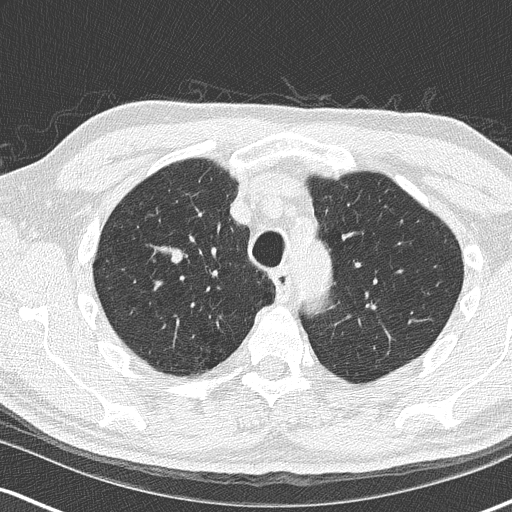
Axial slice from a low-dose chest CT screening exam, second screening round (one year after baseline), lung window (W 1500 / L -600 HU), 2 mm slice thickness, 120 kVp. Male, age 68 years at enrolment.
Expert-annotated lung lesion, bounding box [x1, y1, x2, y2] px = [152, 232, 215, 293]. Screening reader's record for this exam (one nodule recorded; not confirmed to be the boxed lesion): non-calcified nodule or mass ≥4 mm, right upper lobe, 18 × 15 mm, smooth margins, soft tissue attenuation, pre-existing on the prior screen: no. Official screen result: positive, change unspecified: nodule(s) >= 4 mm or enlarging nodule(s), mass(es), or other non-specific abnormalities suspicious for lung cancer. Lung cancer was diagnosed 136 days after this screen: small cell carcinoma, NOS, right upper lobe, stage IIIB (AJCC 6th edition), 20 mm at pathology.